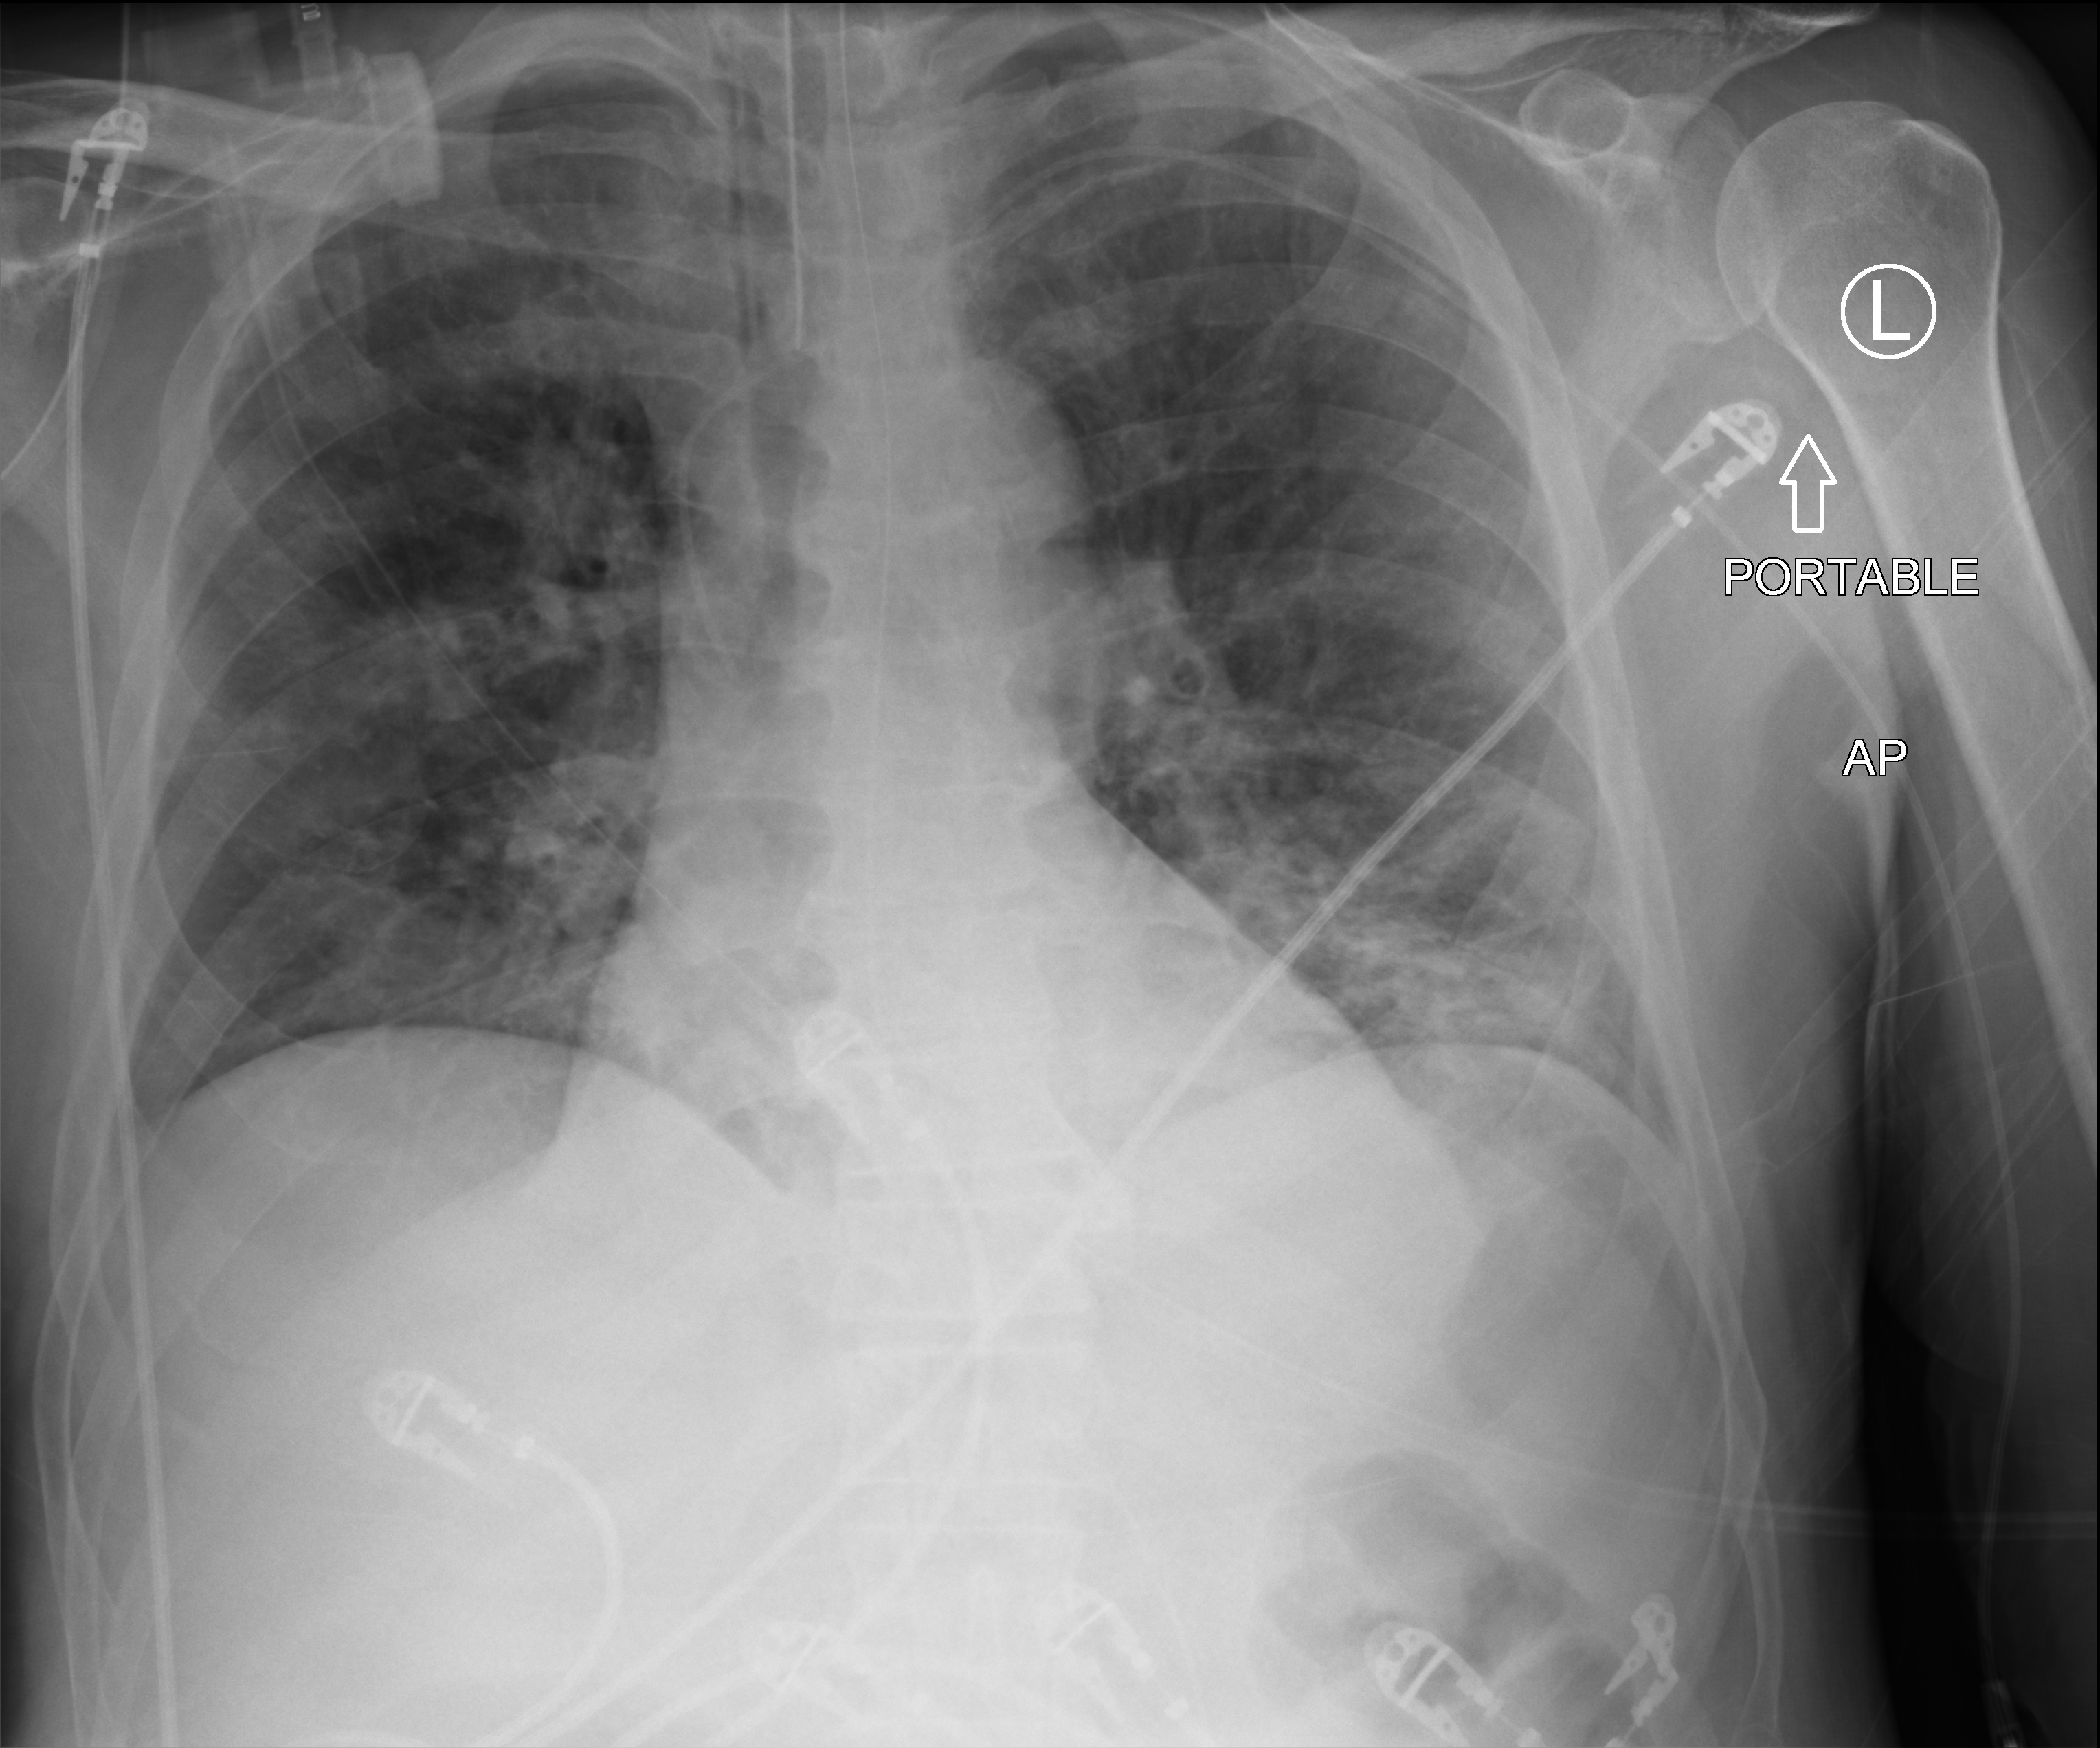
Chest X-ray (portable). Male patient hospitalised with COVID-19, age 60–74 years.
Hospital-stay facts (about this admission, not read from this image; timing relative to this image not recorded): COPD (admission record): no; mechanically ventilated during this hospital stay: yes.